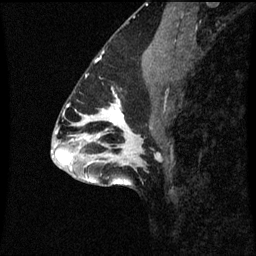
Breast MRI (dynamic contrast-enhanced), one sagittal slice. Position 33 of 60 along the scan axis. Dynamic contrast-enhanced series, image 2 of 3 at this slice position (ordered by acquisition). 1.5 T. TE 4.2 ms, TR 8.9 ms. 2 mm slice thickness. 256 × 256 image matrix, field of view 200 × 200 mm. Patient: female, 43 years. Case-level facts recorded for this patient, not image findings: setting: breast cancer imaged before/during neoadjuvant chemotherapy; receptor status: HR-positive, HER2-negative.
Annotated regions visible in this slice (semi-automatically segmented with operator editing):
- analysis volume of interest (the breast-tissue region the enhancement analysis was run in; not a lesion): box from (x=96, y=96) to (x=159, y=159) px
- tumour enhancement mask (voxels above the 70 % enhancement threshold inside the analysis volume of interest): (x=102, y=96)–(x=125, y=125)